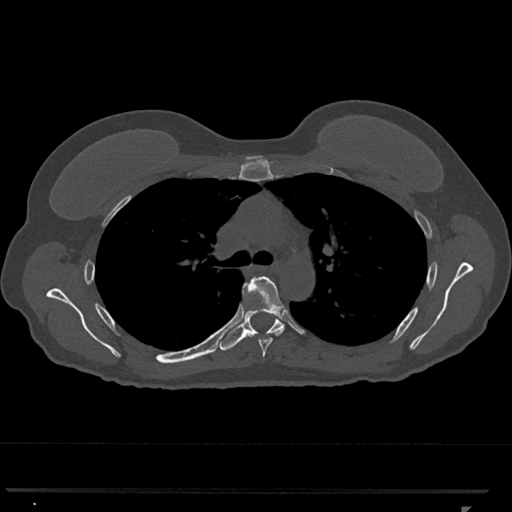
CT including the spine, one axial slice. Slice 785 of 793 in the series (ordered by position). 120 kVp. Bone window (W 1800 / L 400 HU). 0.5 mm slice thickness. 512 × 512 image matrix, field of view 380 × 380 mm. Female patient, age 62 years. Case-level facts recorded for this patient, not image findings: primary cancer: renal.
Outlined on this slice (semi-automatic segmentation, software-assisted and operator-edited):
- T5 vertebra: bounding box <243,276,285,357> (left, top, right, bottom; pixels)
- T6 vertebra: <219,282,284,351>